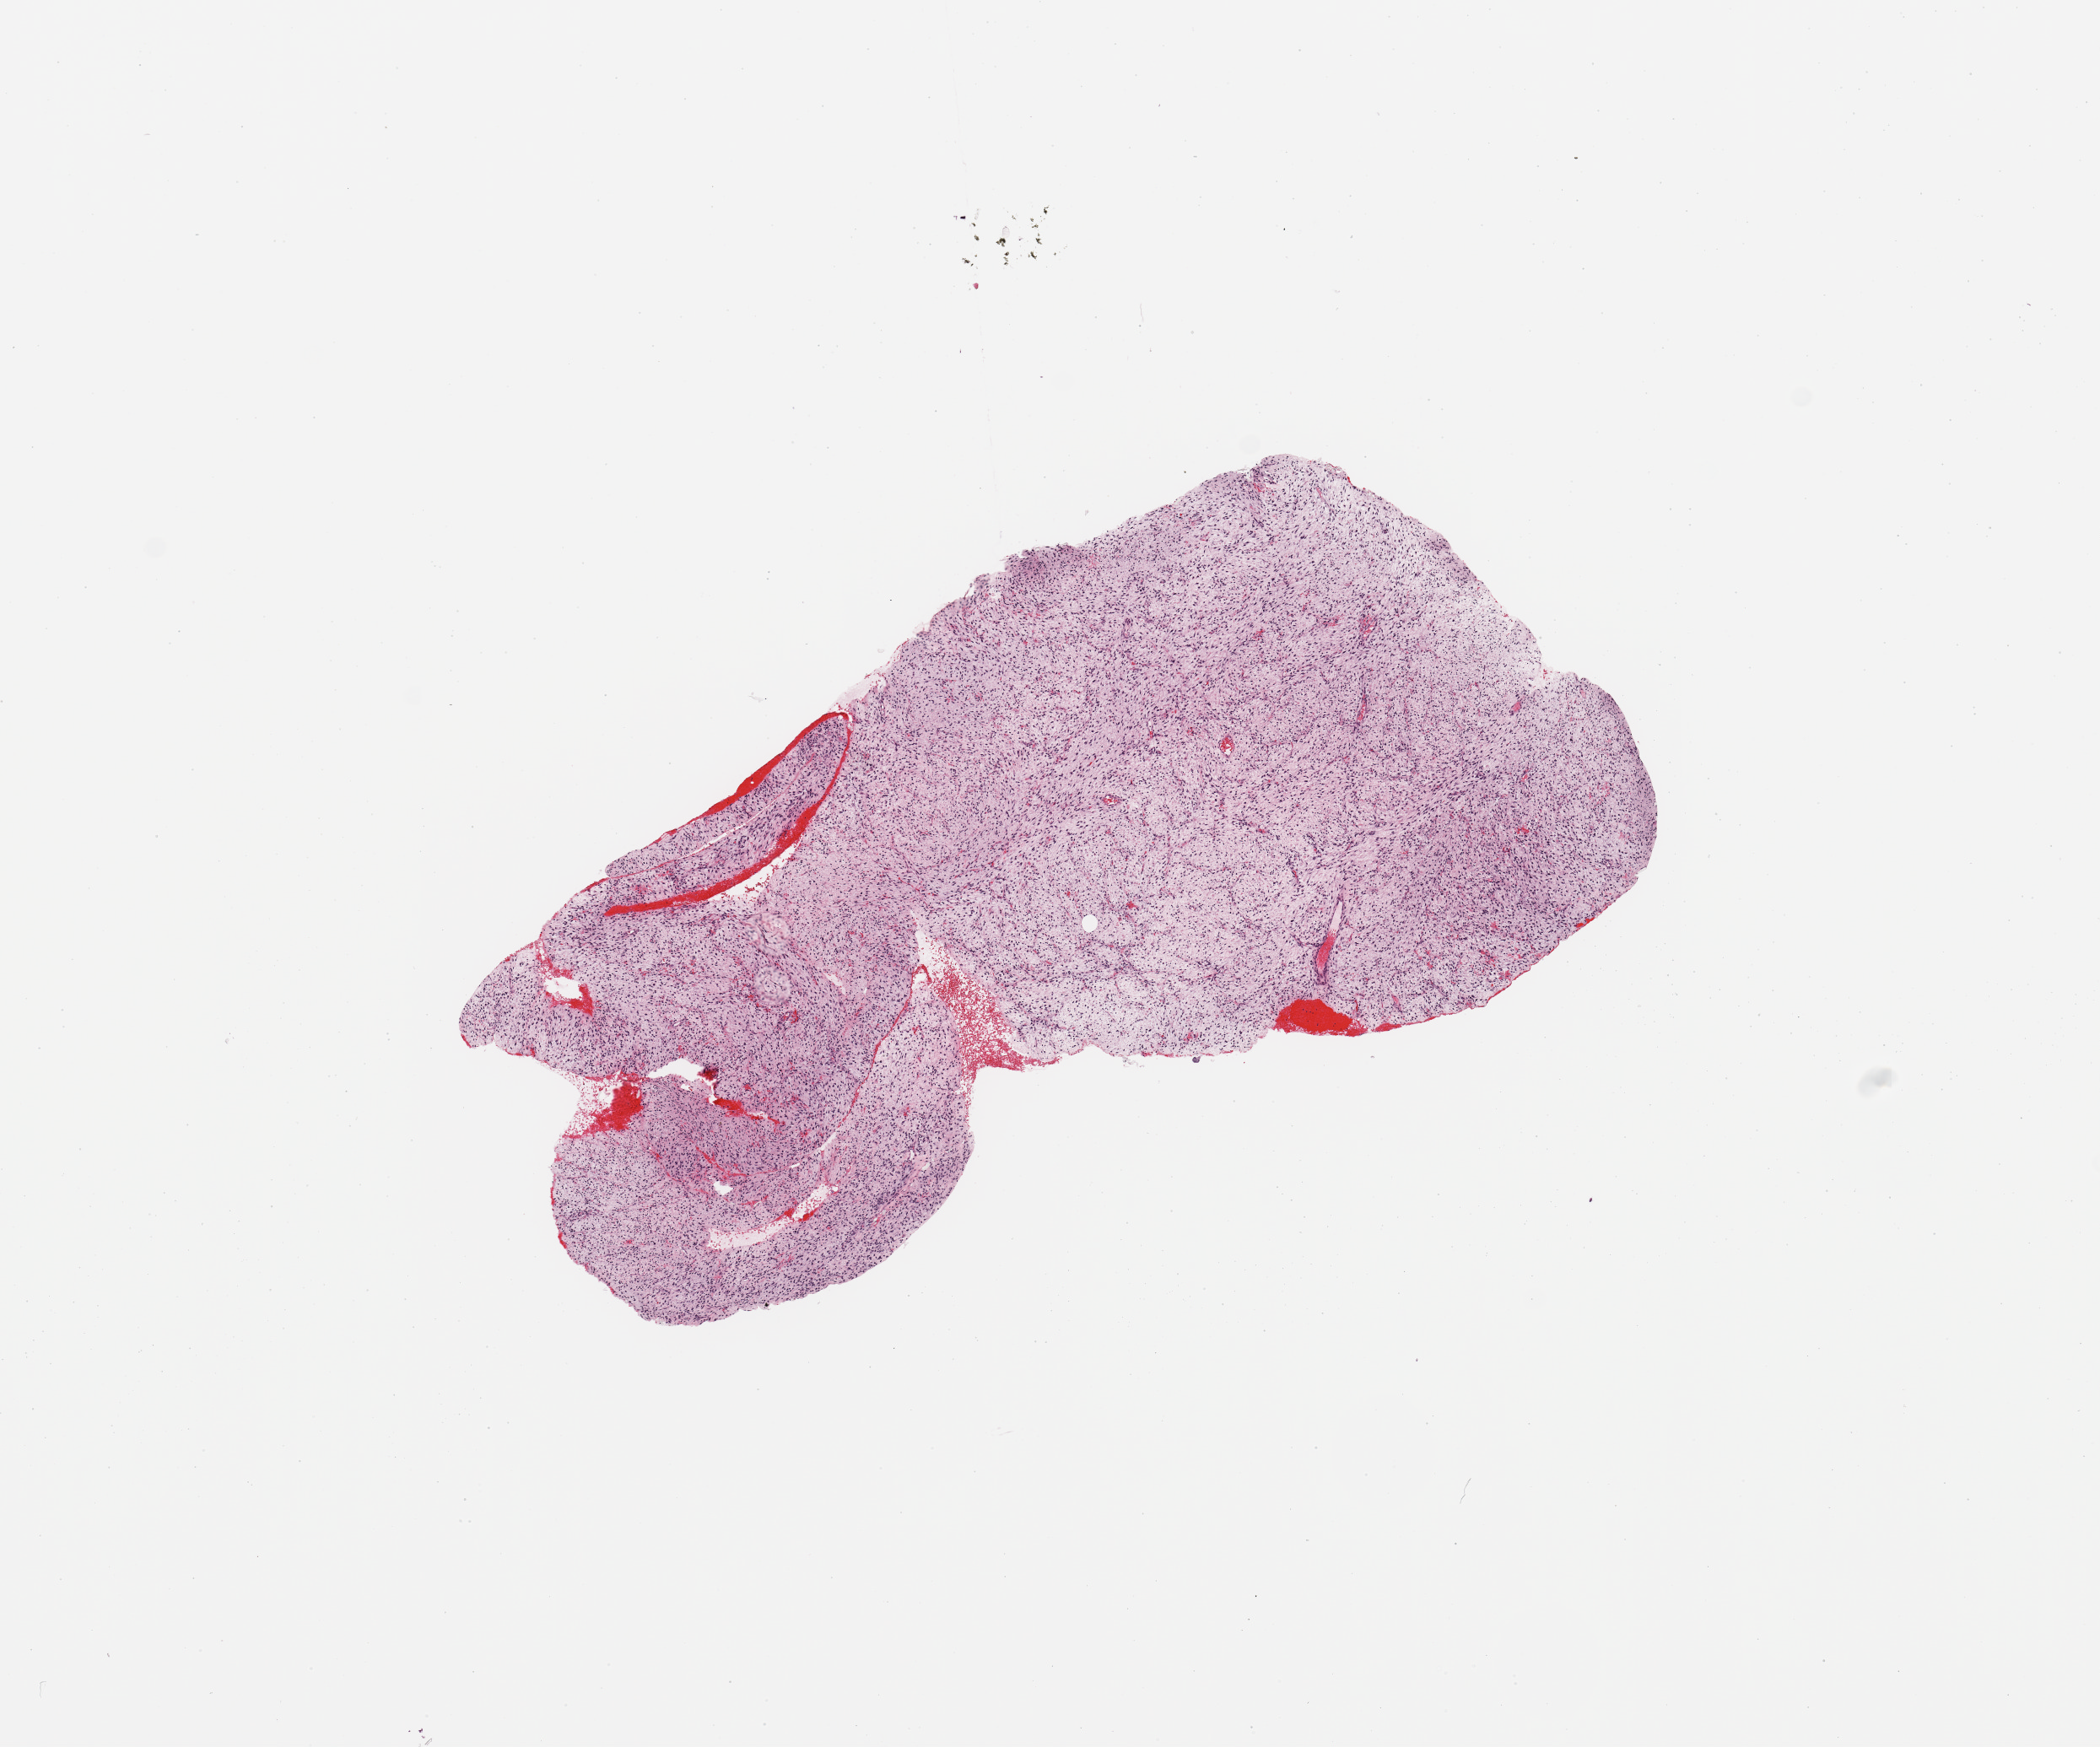
H&E whole-slide image — shown as a low-resolution overview of the whole scanned area (about 9.8 x 8.2 mm), tumour tissue sample. Patient sex: male.
Patient diagnosis (cohort enrolment): sarcoma (site not recorded at cohort level).